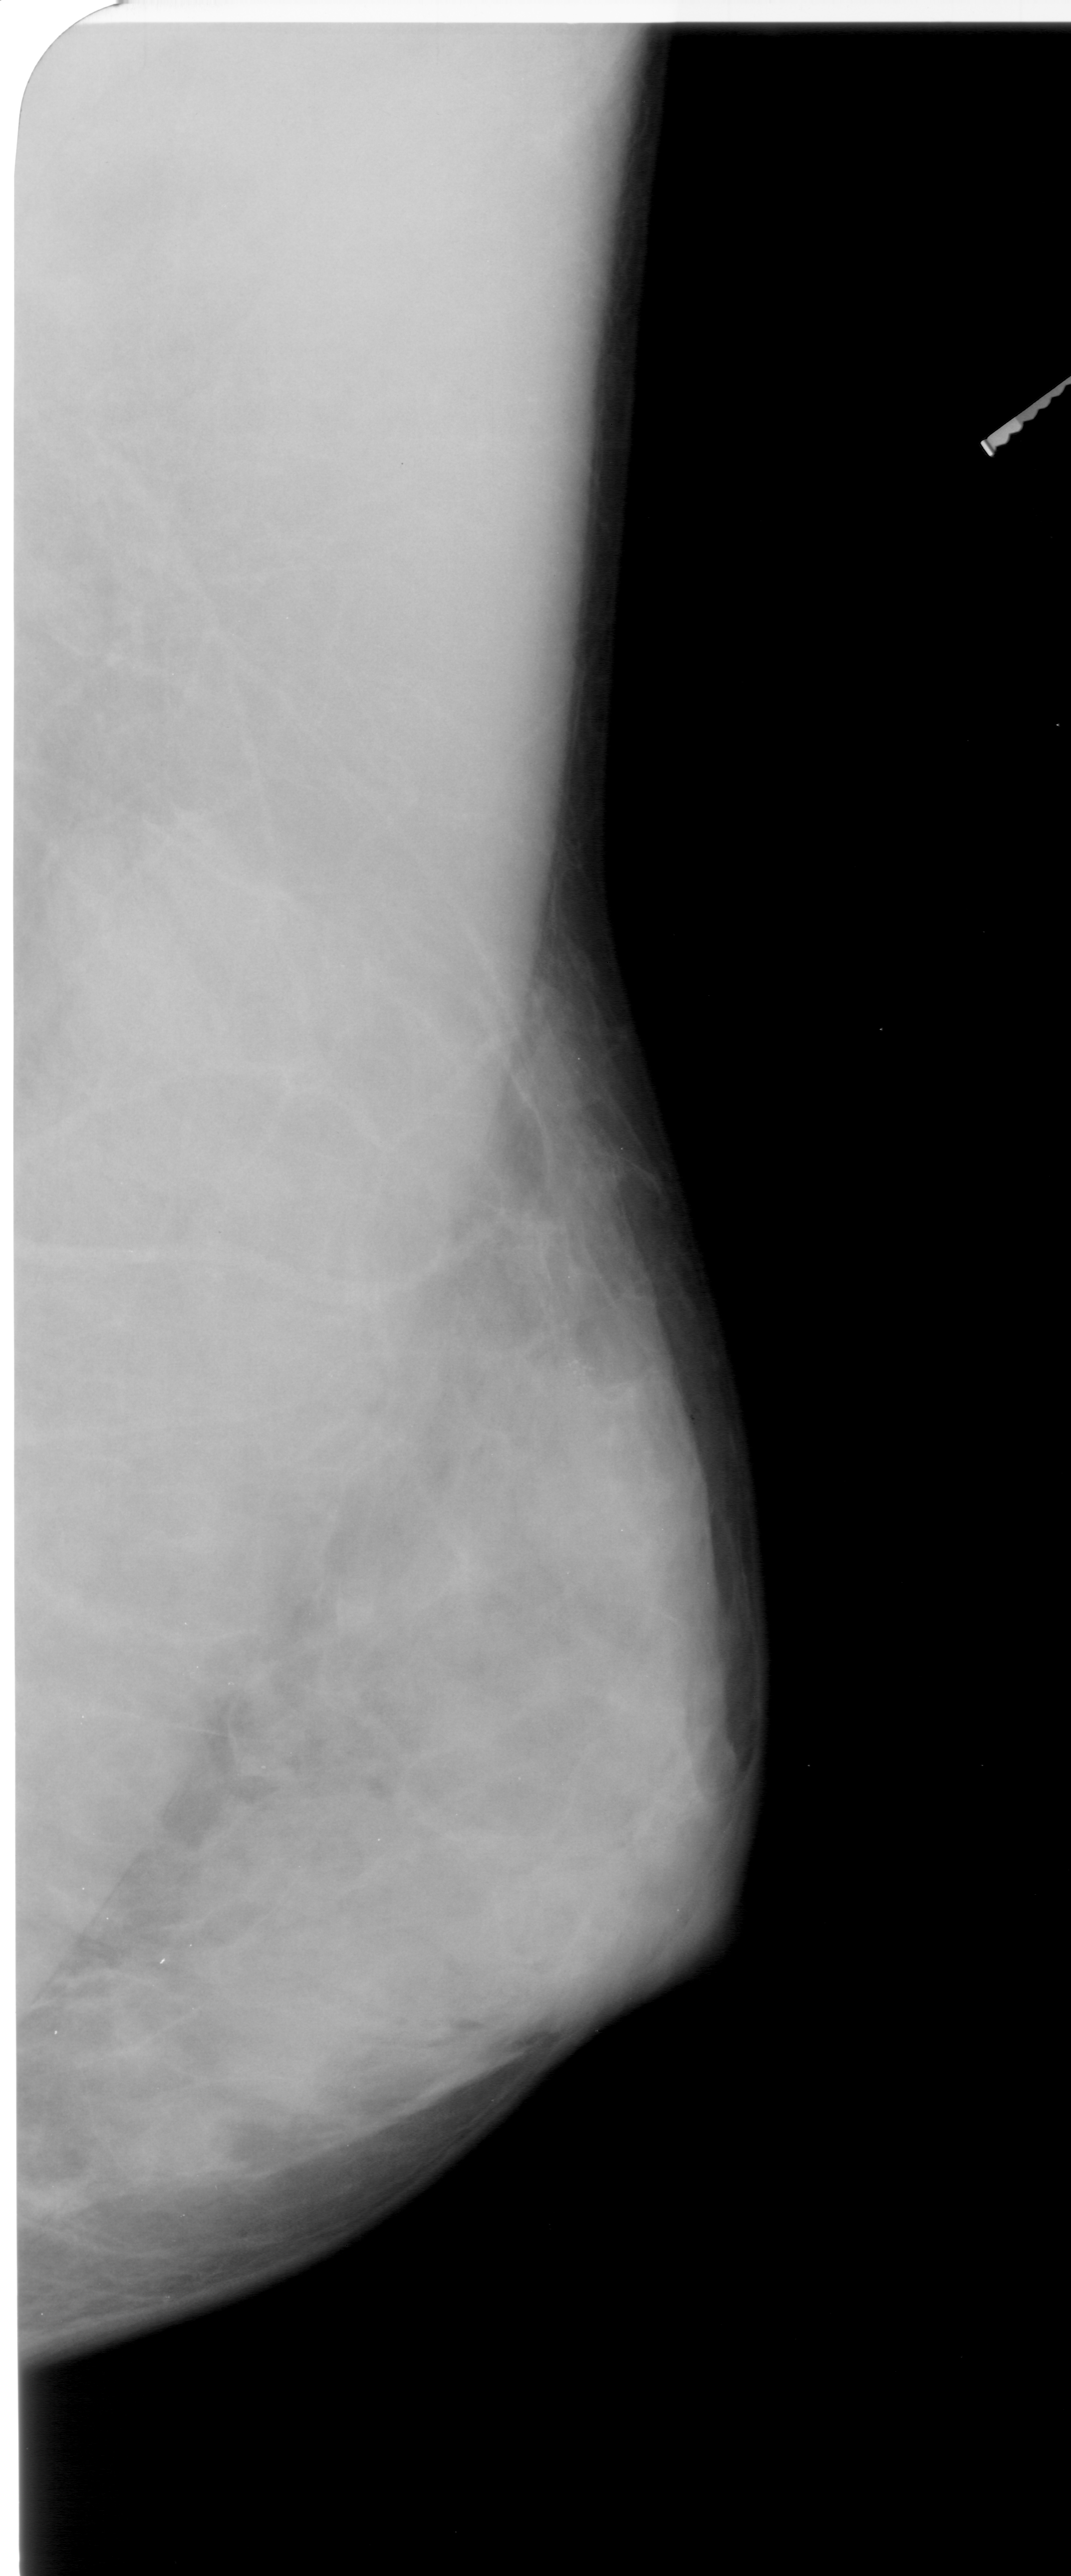
Mammogram (digitized film); right breast; mediolateral oblique (MLO) view; BI-RADS breast density category 4 (scale 1–4); 1071 × 2576 image matrix.
Expert-marked regions of interest on this image (one box per marked abnormality):
- calcifications, morphology pleomorphic, distribution clustered; BI-RADS assessment category 4; pathology (as recorded): benign: box from (x=477, y=1279) to (x=678, y=1476) px